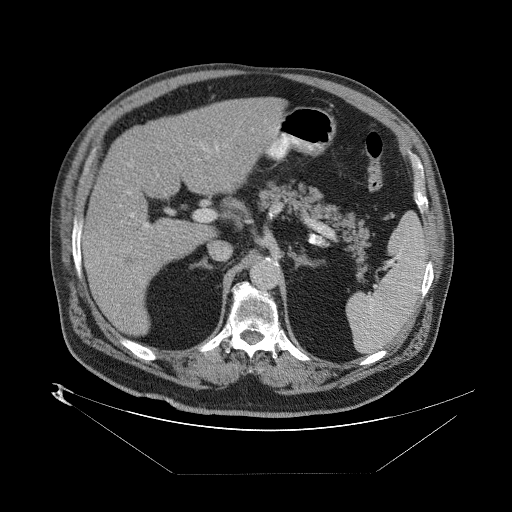
Contrast-enhanced abdominal CT (liver protocol), one axial slice. Position 43 of 89 along the scan axis. One of 2 acquisitions stored at this slice position. Soft-tissue window (W 400 / L 40 HU). 2.5 mm slice thickness. 512 × 512 image matrix, field of view 480 × 480 mm. From the clinical record (not read from this slice): diagnosis: hepatocellular carcinoma (patient treated with transarterial chemoembolisation; whether this scan precedes or follows treatment is not stated here); TNM stage (as recorded): Stage-II; Child-Pugh class: B.
Outlined on this slice (semi-automatically segmented with operator editing):
- abdominal aorta: bounding box [x1, y1, x2, y2] px = [251, 260, 278, 288]
- liver parenchyma outside the tumour (the mass and vessels are separate outlines, so this box may not span the whole liver): [84, 94, 283, 338]
- mass: [120, 249, 138, 268]
- liver vessels: [91, 140, 227, 284]